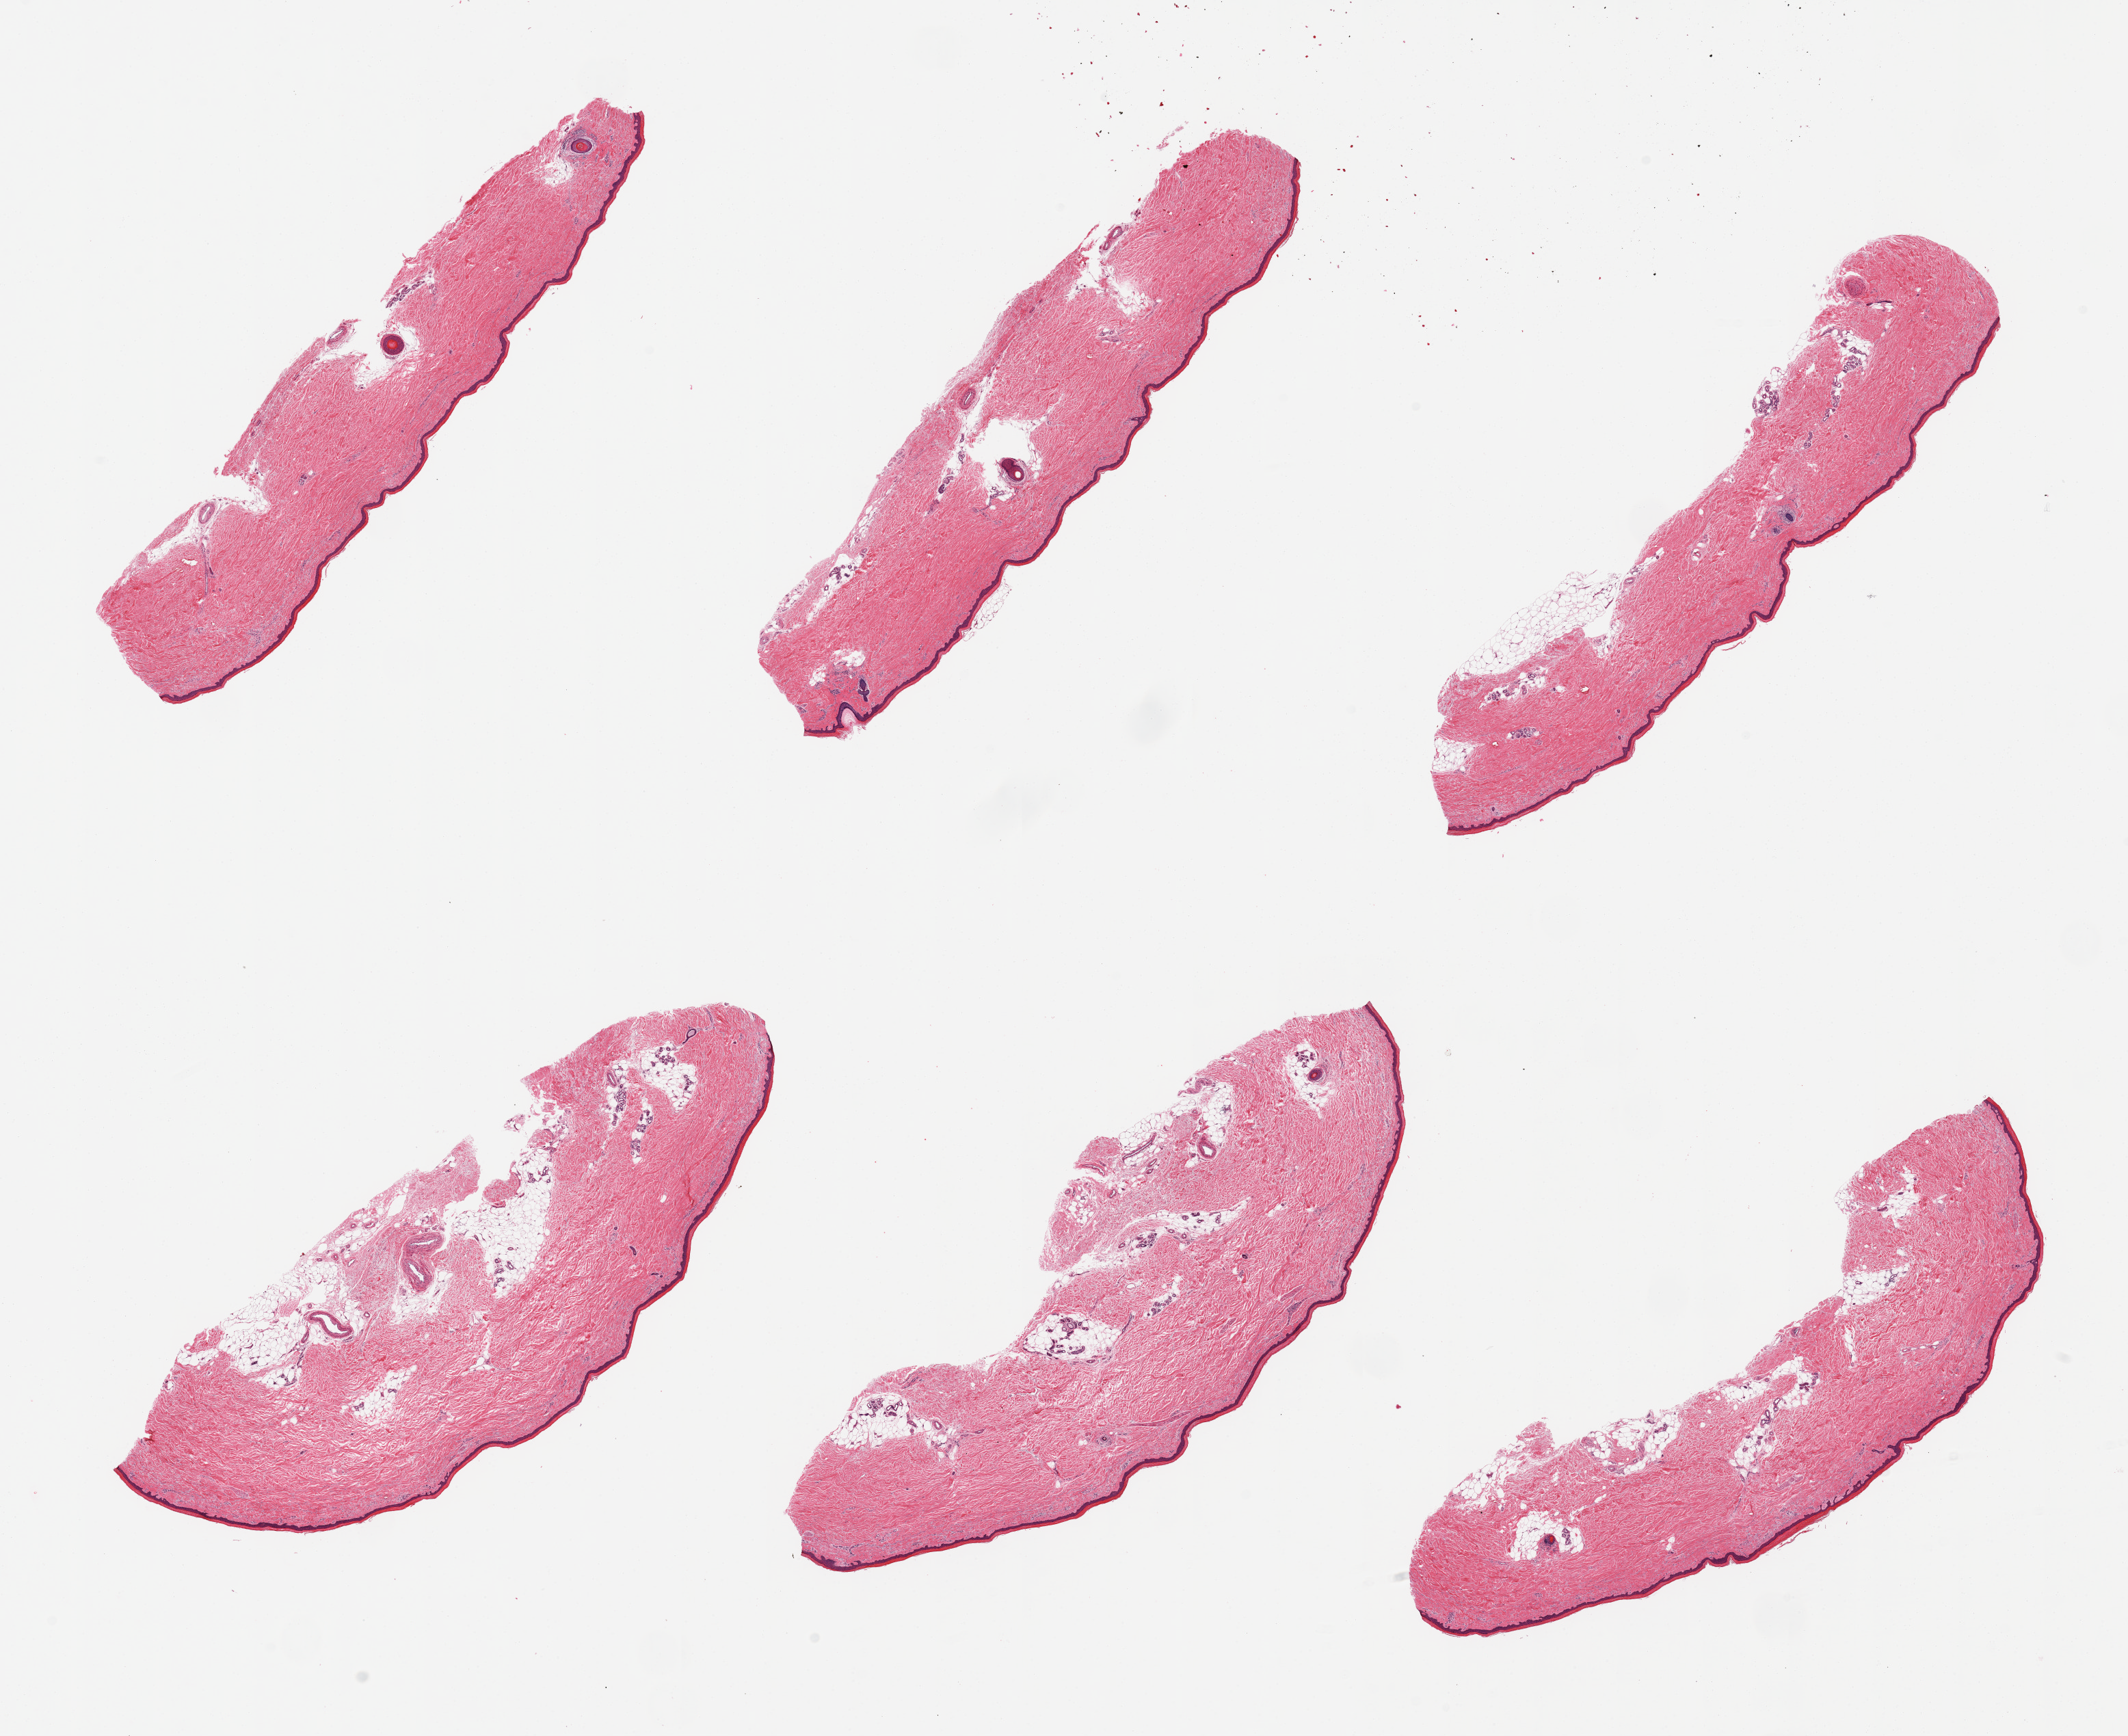
H&E whole-slide image, shown as a low-resolution overview of the whole scanned area (about 24.6 x 20.1 mm, slide scanned at 20x), PAXgene-fixed paraffin-embedded (PFPE) section, section of skin of lower leg (target tissue), donor tissue sample. Donor sex: female.
Reviewer comment on this tissue sample: 6 pieces, no significant dermal fat; squamous epithelium is ~50-60 microns.